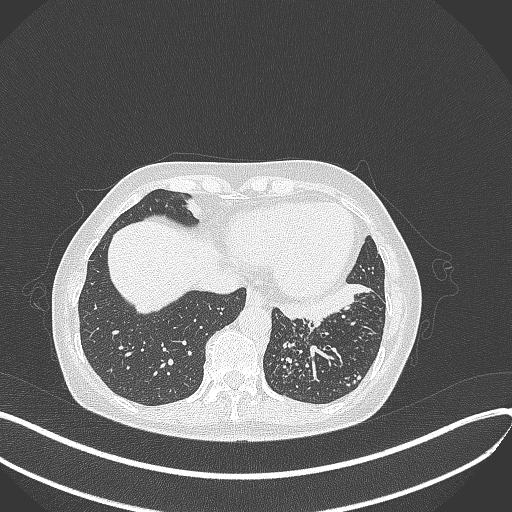
Chest CT, one axial slice; slice 108 of 429 in the series (ordered by position); reconstruction kernel B70f; lung window (W 1500 / L -600 HU); 1 mm slice thickness; 512 × 512 image matrix, field of view 400 × 400 mm. Female patient, age 63 years. Case-level facts recorded for this patient, not image findings: clinical TNM (as recorded): T1b N0 M0; histopathological grade: G2-3.
Outlined on this slice (bounding box drawn by a radiologist):
- lung tumour (recorded histology: adenocarcinoma): bounding box <281,282,373,327> (left, top, right, bottom; pixels)